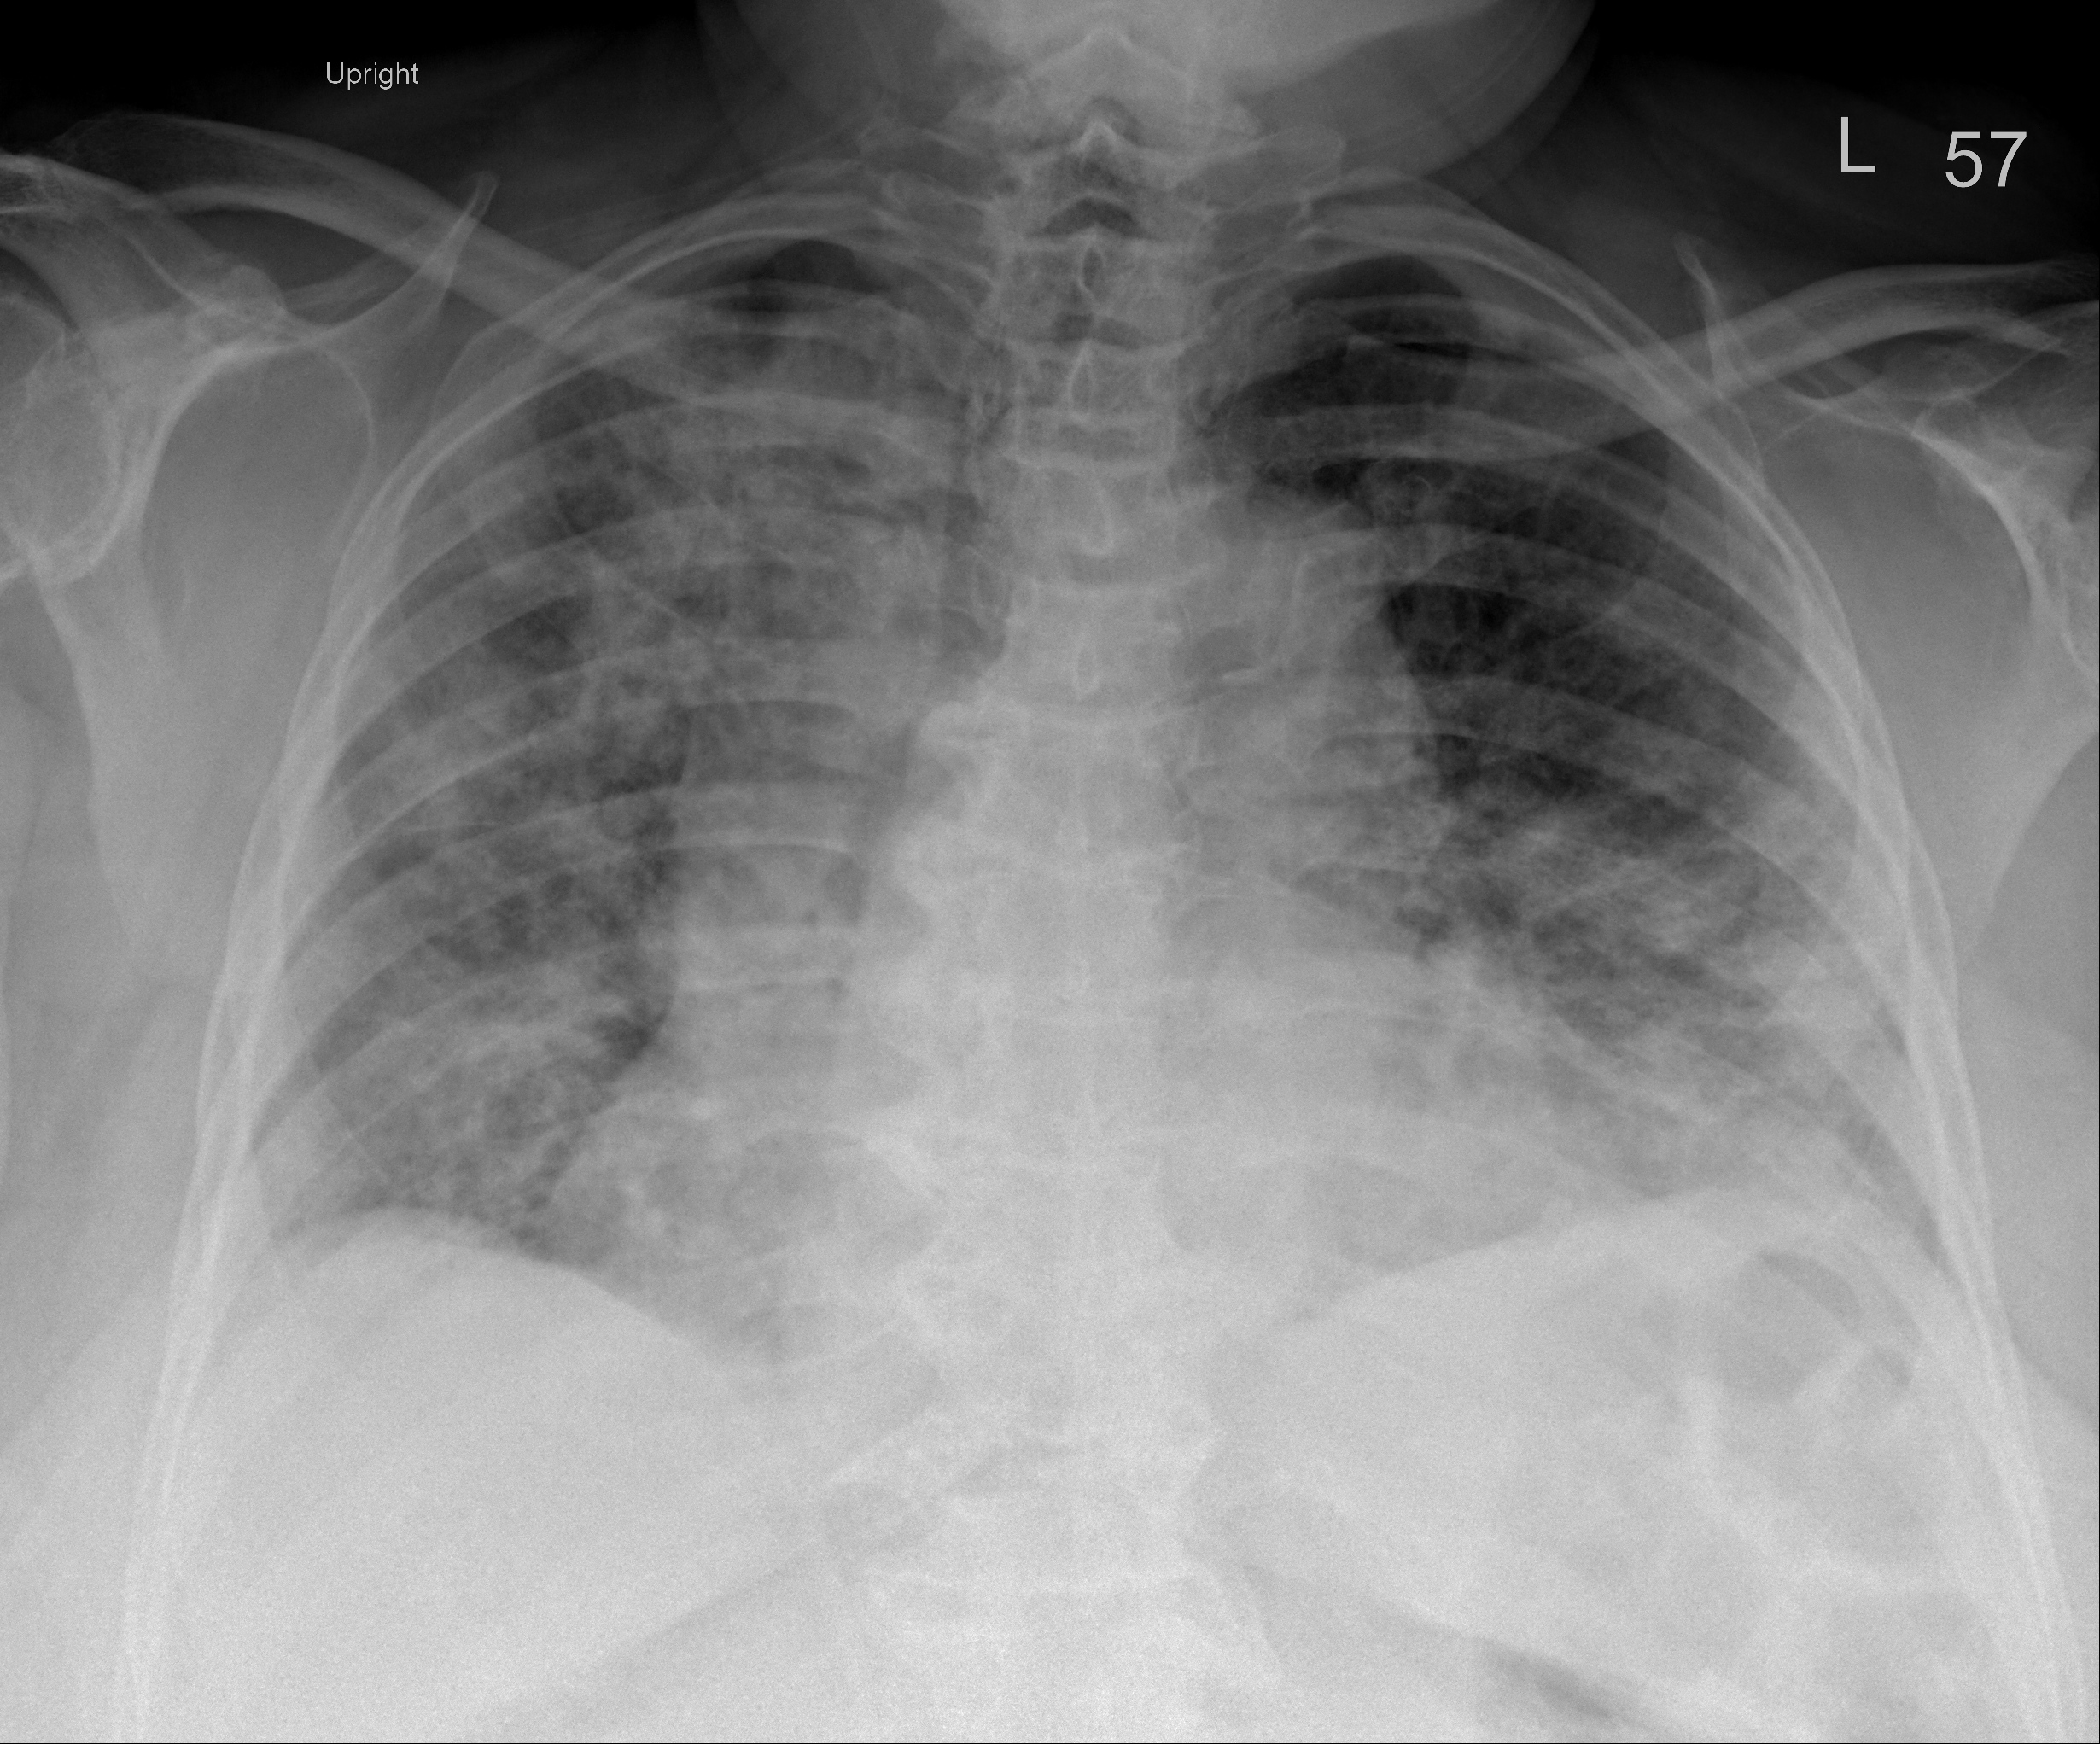
Portable chest radiograph, AP projection. Female patient, age 73 years; COVID-19 (test-positive).
Radiologist key findings (as recorded): some worsening of now somewhat more diffuse airspace disease. Airspace disease is increased in right upper lobe. Left upper lobe however spared. Persistent airspace disease seen in both lower lobes.